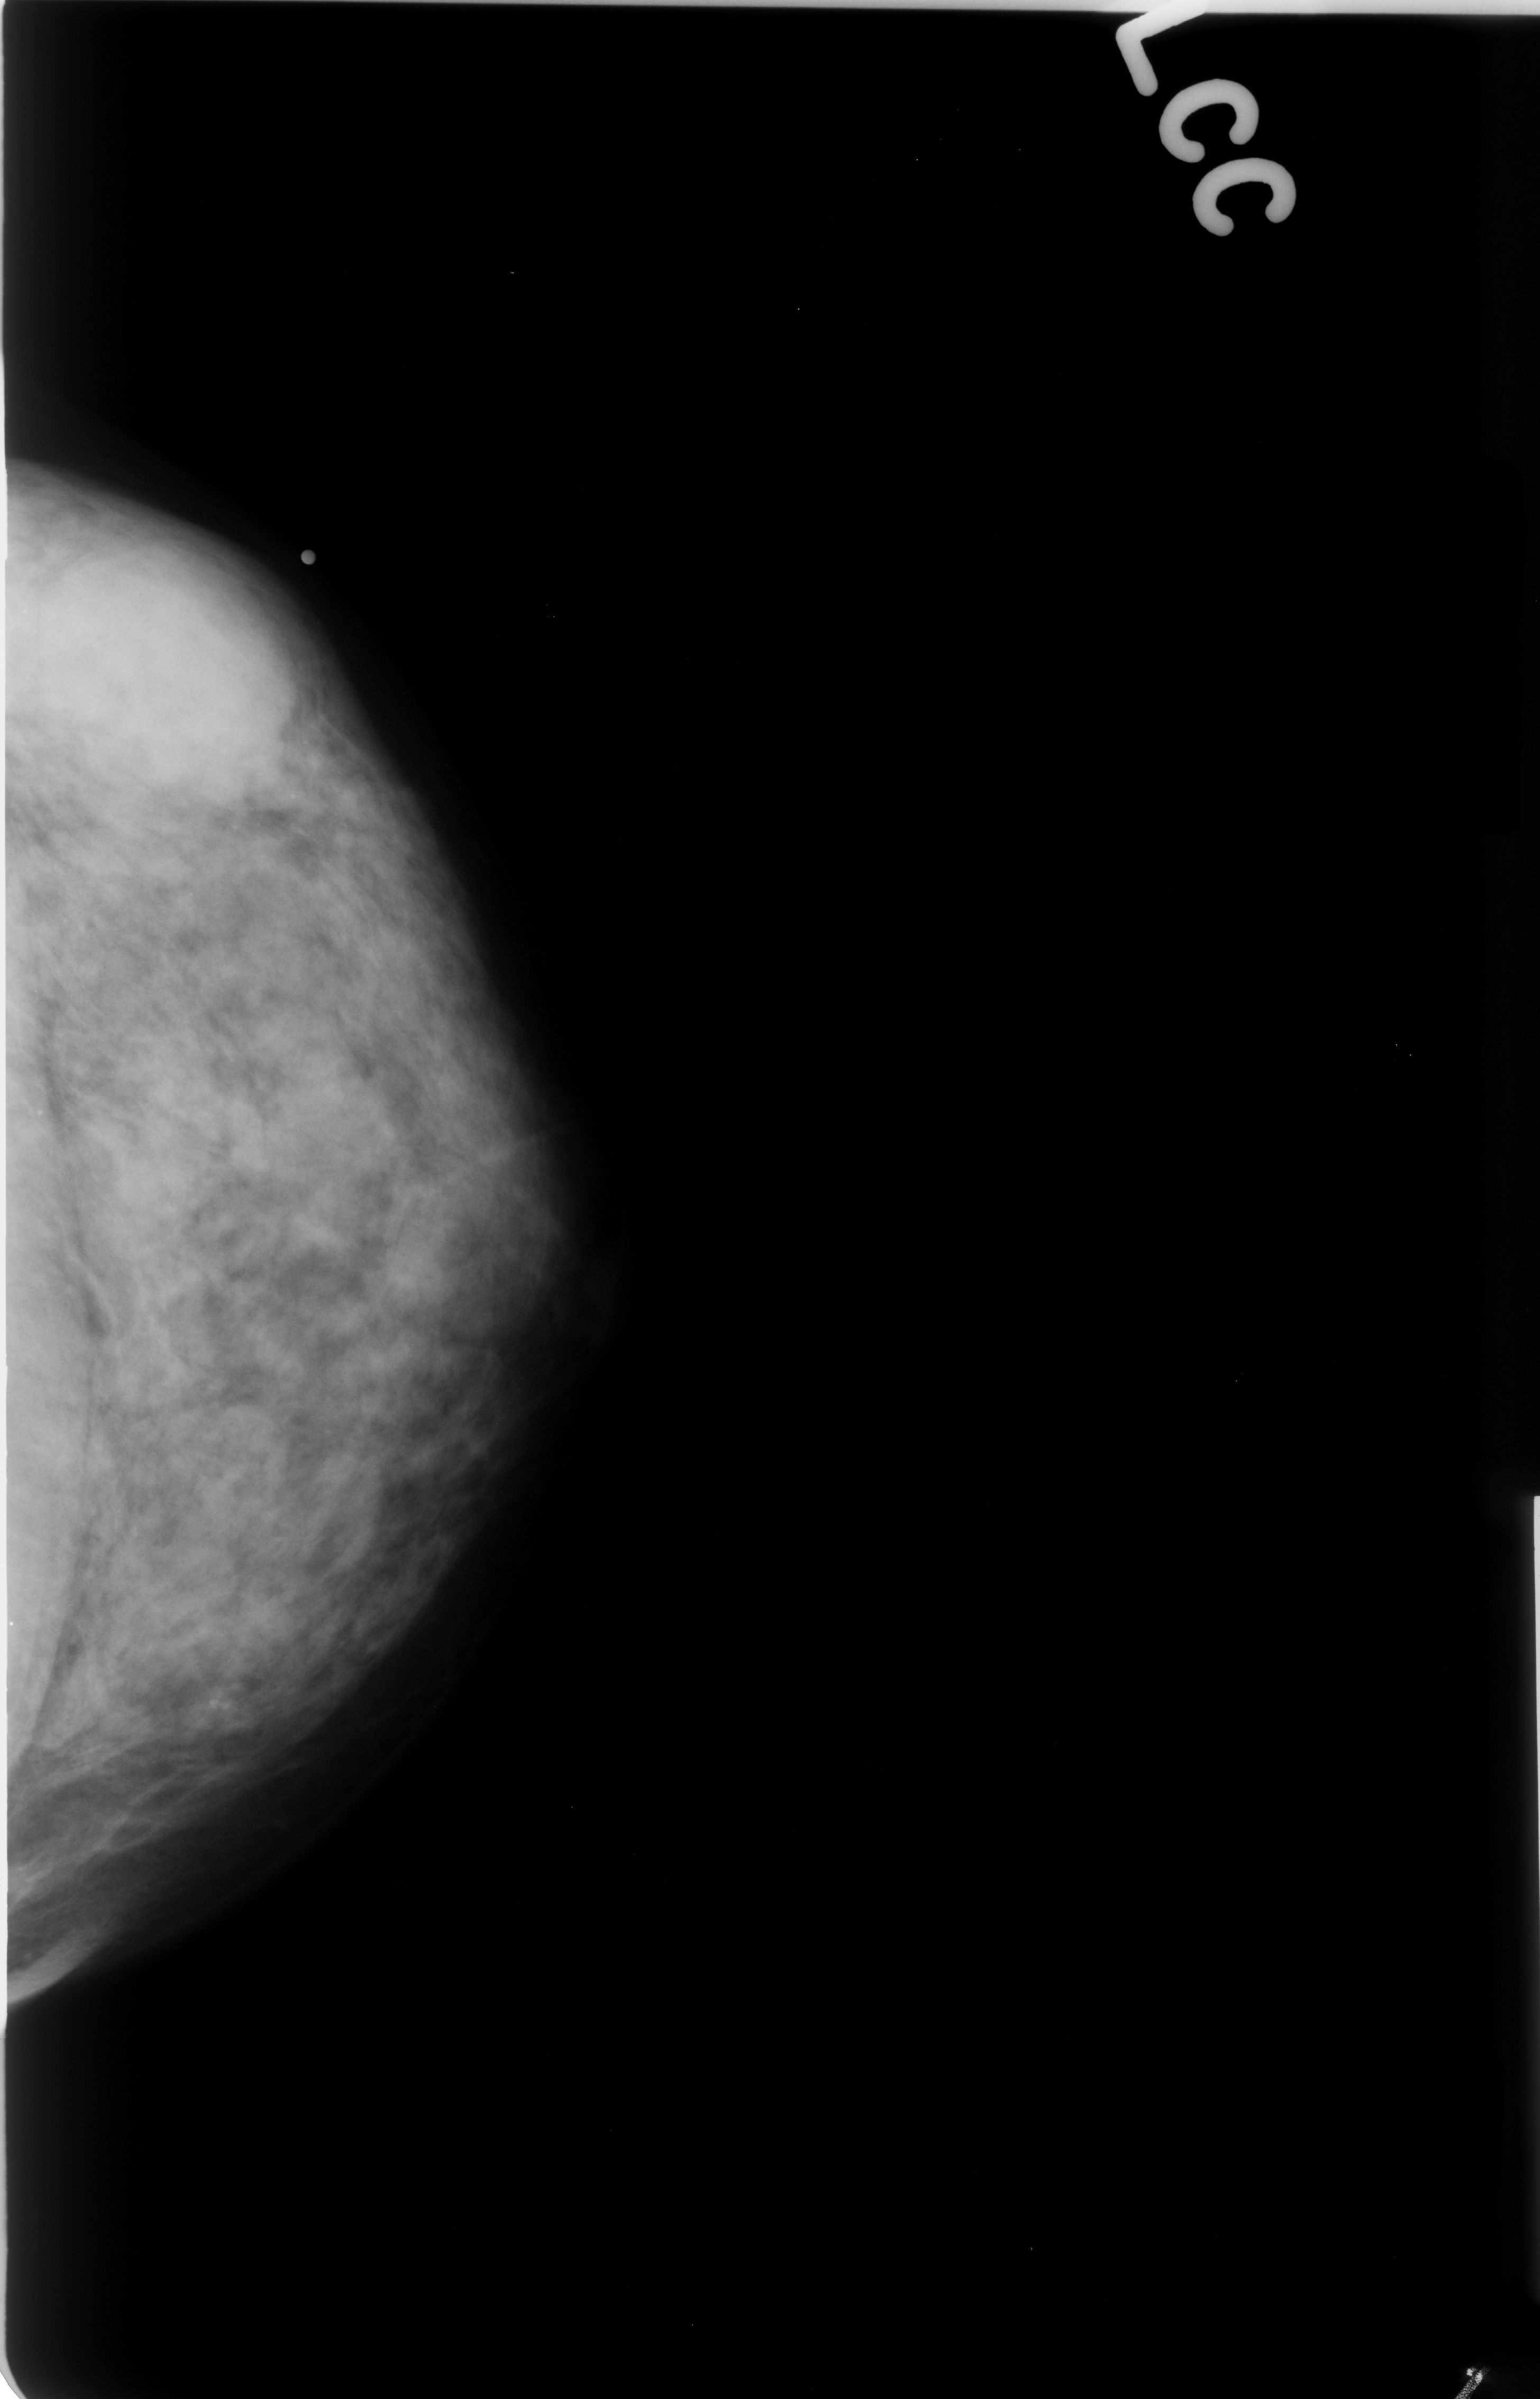
Scanned film-screen mammogram; left breast; craniocaudal (CC) view; BI-RADS breast density category 3 (scale 1–4); 1540 × 2399 image matrix.
Expert-marked regions of interest on this image (one box per marked abnormality):
- calcifications, morphology dystrophic, distribution clustered; BI-RADS assessment category 3; subtlety rating 3 on a 1 (subtle) to 5 (obvious) scale; pathology (as recorded): benign: box from (x=173, y=1641) to (x=289, y=1761) px